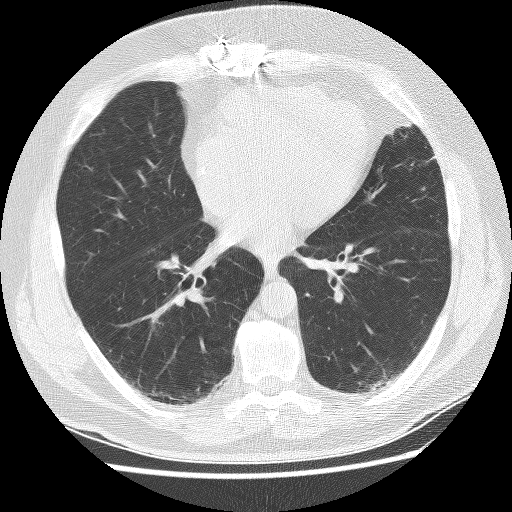
Chest CT (low-dose screening protocol), one axial image. Baseline screening round. Lung window (W 1500 / L -600 HU). 2.5 mm slice thickness. Lung (sharp) reconstruction kernel (BONE). Slice 132 of 236 in the series. 512 × 512 image matrix. Male, age 65 years at enrolment.
Expert reader's lesion annotation, bounding box <354,371,395,407> (left, top, right, bottom; pixels). No non-calcified nodule or mass ≥4 mm was recorded by the screening reader at this exam. Official screen result: negative screen, minor abnormalities not suspicious for lung cancer. Later outcome: lung cancer diagnosed 523 days after this screen — squamous cell carcinoma, NOS, left lower lobe, moderately differentiated (G2), stage IA (AJCC 6th edition), 20 mm at pathology.